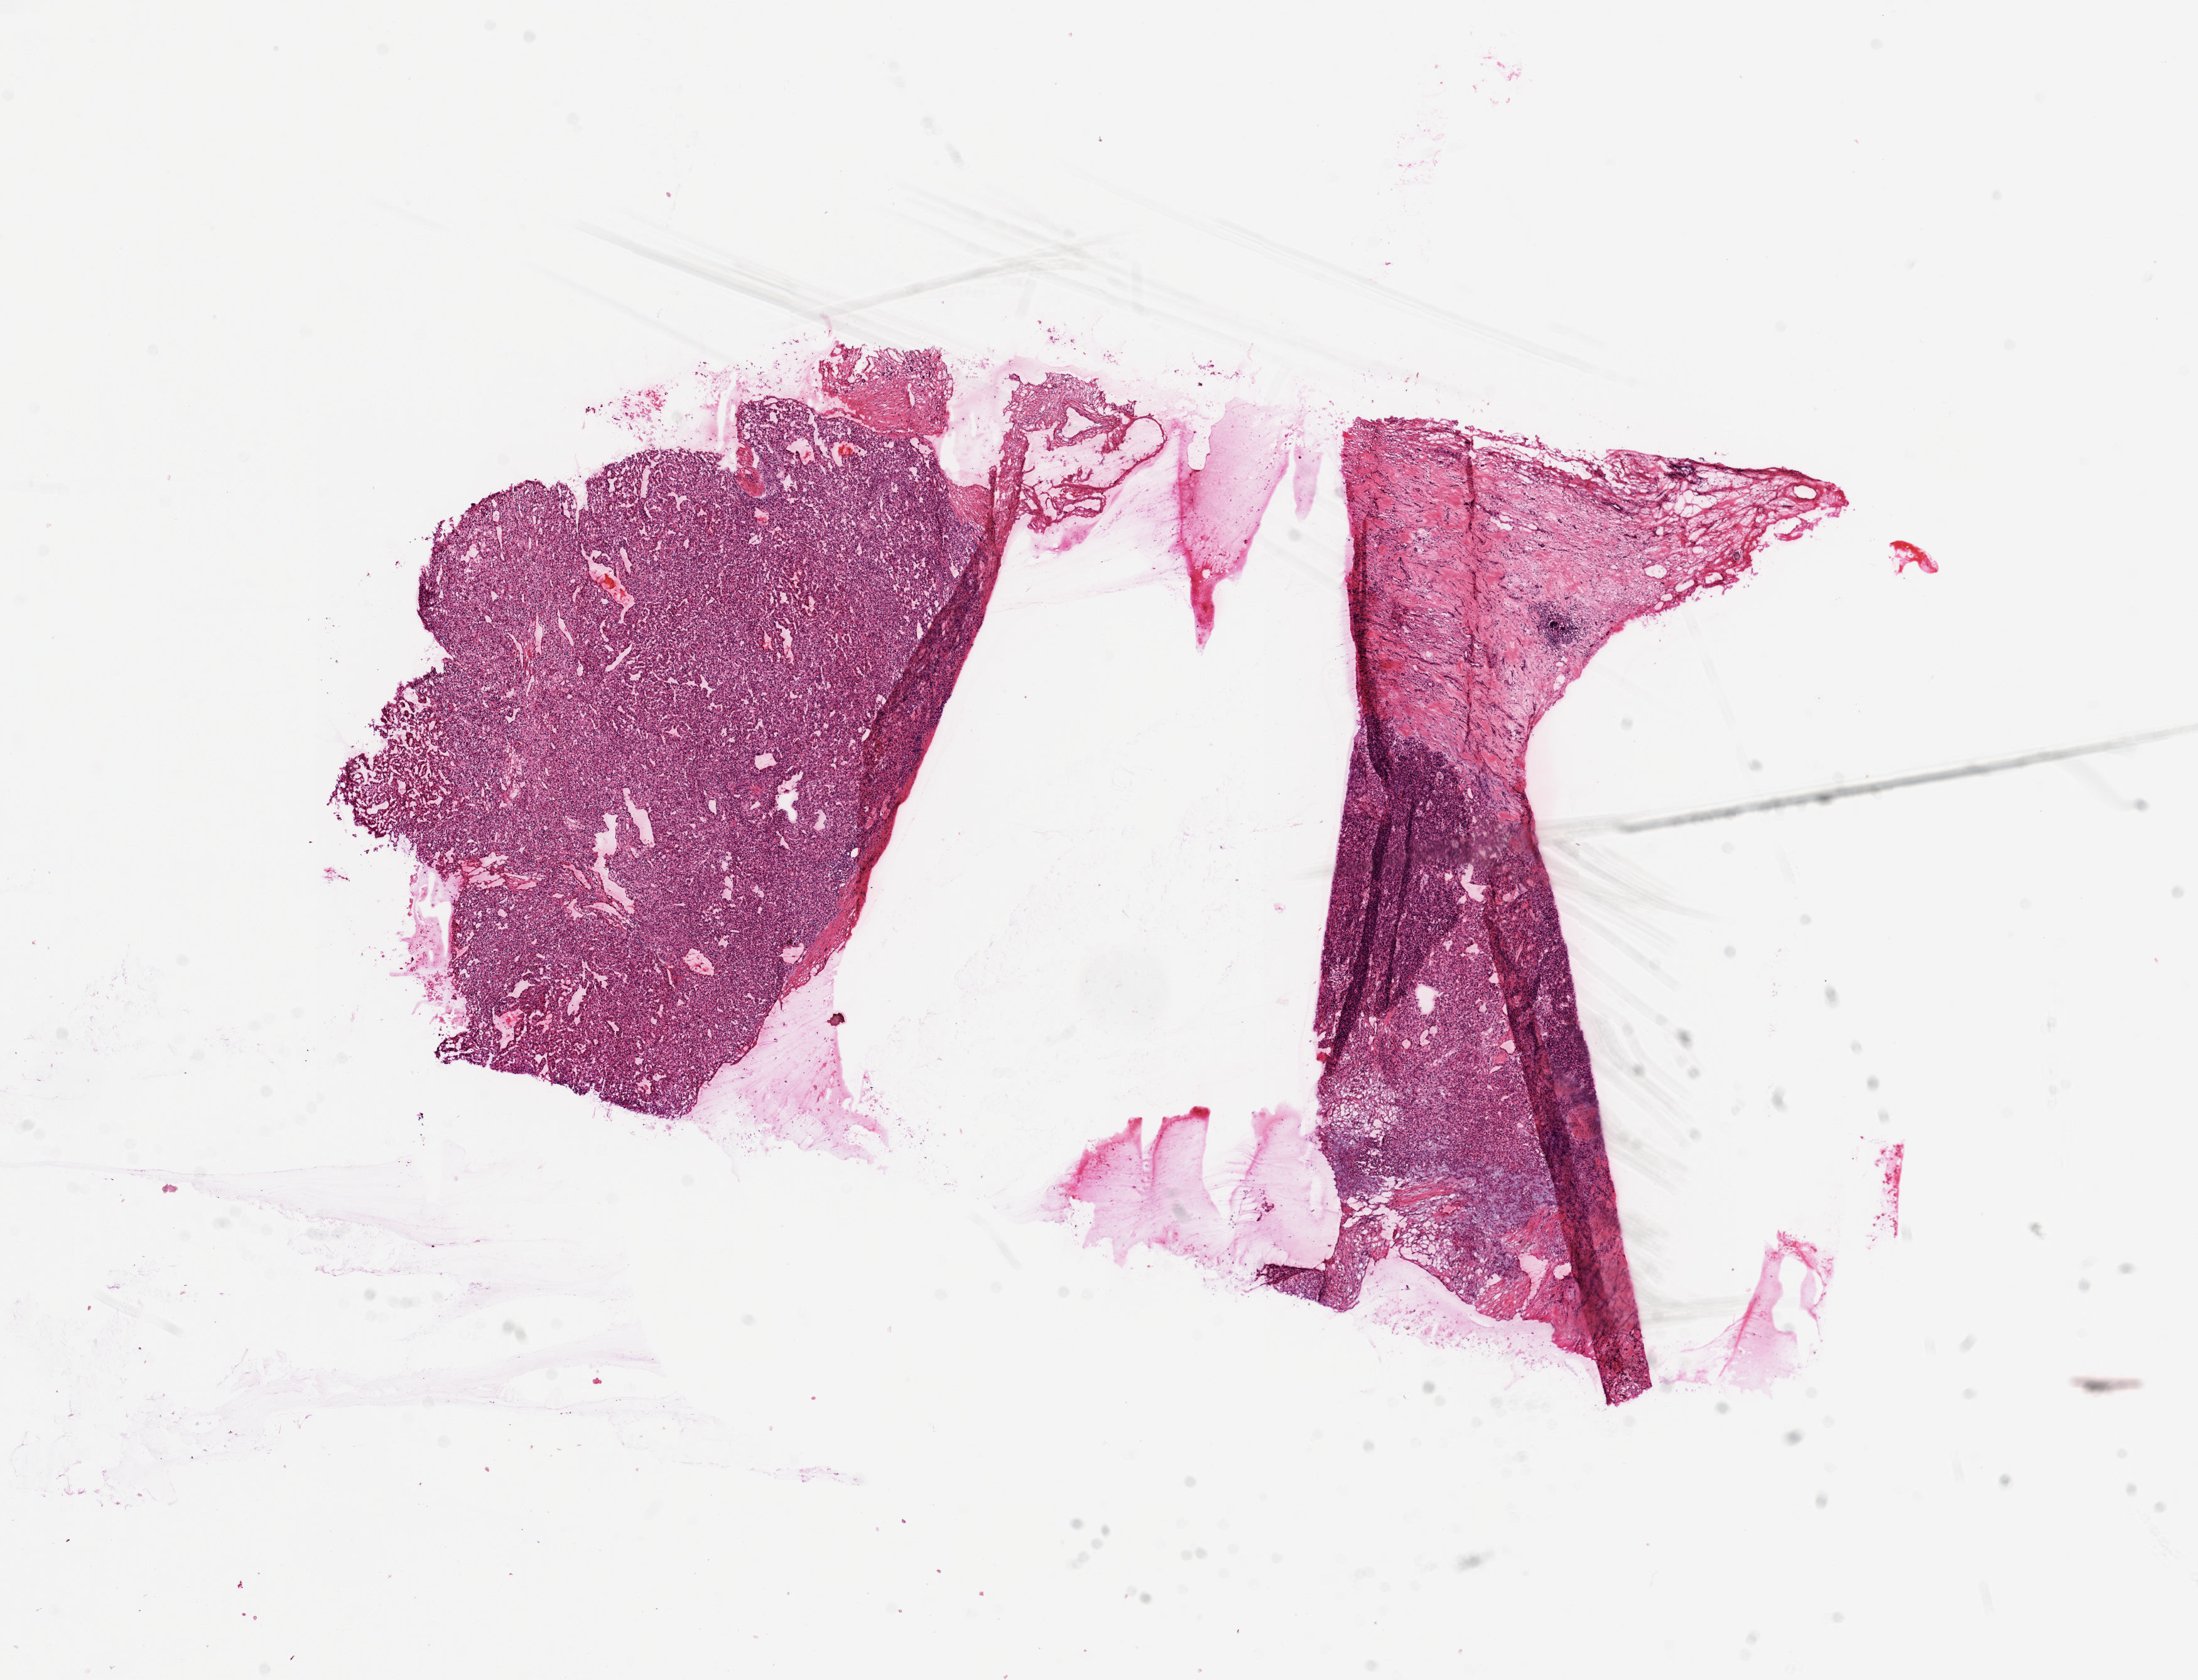
H&E whole-slide image, low-resolution overview of the scanned area, about 14.0 x 10.7 mm (acquisition: 20x scan). Frozen section from the top of the tissue portion. Sample: primary tumour, kidney. Male patient; age at initial diagnosis 58 years. Histologic grade: G3 (poorly differentiated). Composition of this section per pathologist review: tumour cells 80%, tumour nuclei 85%, normal cells 0%, stromal cells 20%, necrosis 0%.
AJCC pathologic stage: III. Diagnosis: Clear cell adenocarcinoma, NOS.